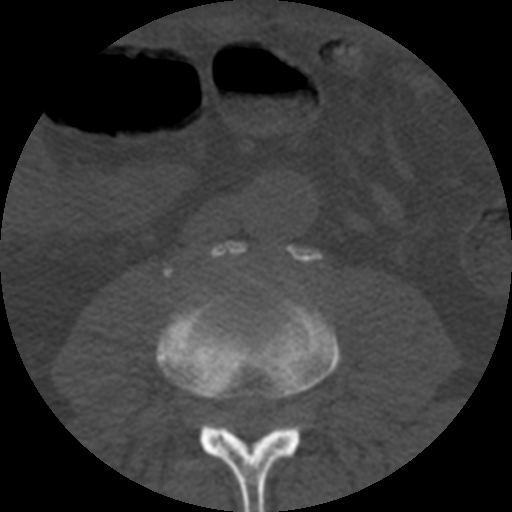
CT including the spine, one axial slice. Position 112 of 508 along the scan axis. Reconstruction kernel STANDARD. 120 kVp. Bone window (W 1800 / L 400 HU). 512 × 512 image matrix, field of view 160 × 160 mm. Patient age 57 years. From the clinical record (not read from this slice): primary cancer: prostate.
Outlined on this slice (semi-automatically segmented with operator editing):
- L3 vertebra: box from (x=156, y=294) to (x=342, y=512) px
- L4 vertebra: (x=212, y=241)–(x=321, y=264)